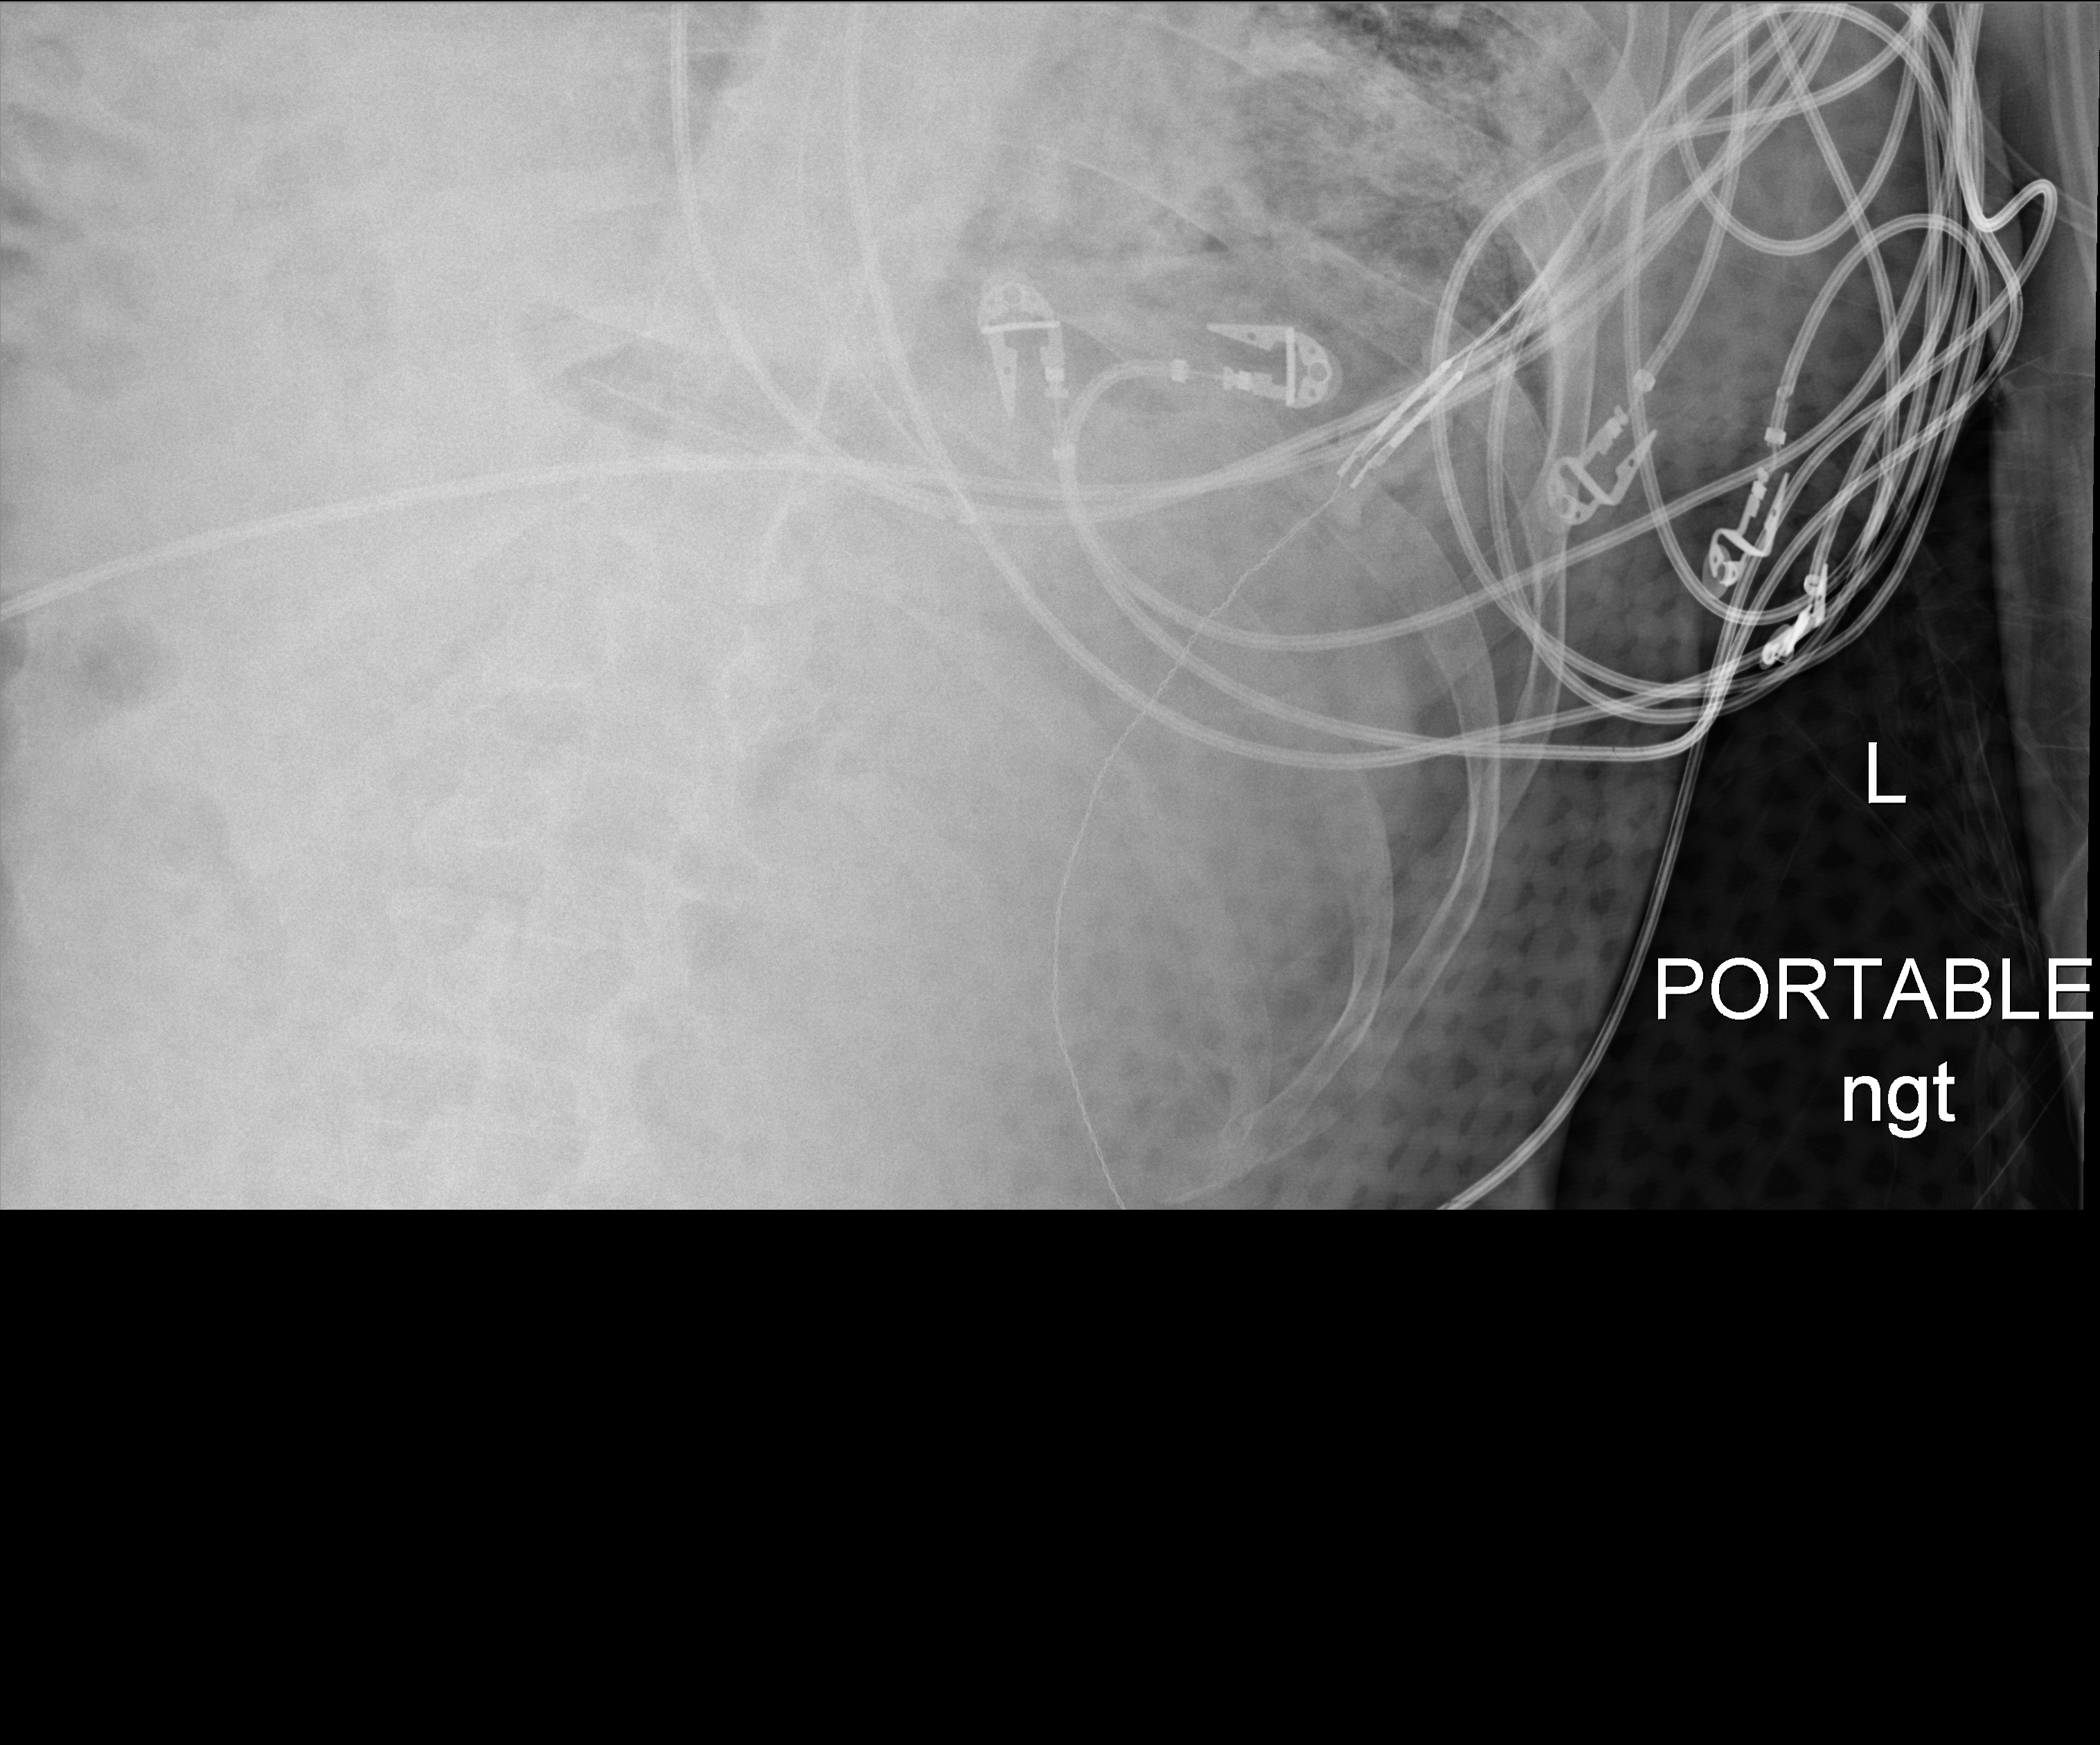
Portable chest radiograph; anteroposterior (AP) projection. Male patient hospitalised with COVID-19, age 18–59 years.
Hospital-stay facts (about this admission, not read from this image; timing relative to this image not recorded): diabetes (admission record): no; admitted to intensive care during this hospital stay: yes.